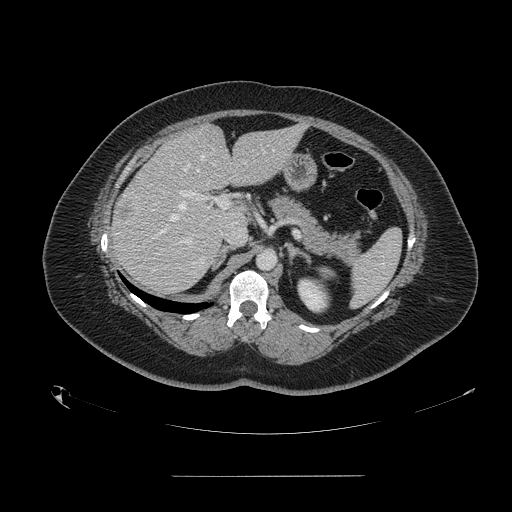
Contrast-enhanced abdominal CT, one axial slice; slice 93 of 164 in the series (ordered by position); 120 kVp; intravenous contrast given; soft-tissue window (W 400 / L 40 HU); 2.5 mm slice thickness; 512 × 512 image matrix, field of view 495 × 495 mm. Female patient, age 52 years. Case-level facts recorded for this patient, not image findings: diagnosis: colorectal cancer liver metastases, imaged before liver resection; multiple liver metastases: yes; largest metastasis: 3.5 cm; chemotherapy before resection: no.
Outlined on this slice (outlined manually by an expert reader):
- hepatic veins: box from (x=153, y=155) to (x=204, y=239) px
- liver: (x=112, y=125)–(x=301, y=293)
- planned liver remnant (the part of the liver to remain after resection): (x=176, y=125)–(x=301, y=227)
- portal vein (with intrahepatic branches): (x=179, y=191)–(x=230, y=244)
- liver metastasis: (x=118, y=201)–(x=131, y=220)